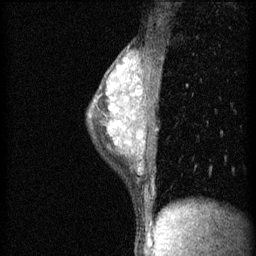
Breast MRI (dynamic contrast-enhanced), one sagittal slice; position 40 of 60 along the scan axis; 3 images stored at this slice position (order not interpretable as contrast timing); 1.5 T; TE 4.2 ms, TR 11 ms; 2 mm slice thickness; 256 × 256 image matrix. Patient: female, 40 years.
Structures marked on this image (semi-automatically segmented with operator editing):
- analysis volume of interest (the breast-tissue region the enhancement analysis was run in; not a lesion): box from (x=88, y=50) to (x=155, y=191) px
- tumour enhancement mask (voxels above the 70 % enhancement threshold inside the analysis volume of interest): (x=140, y=92)–(x=142, y=95)